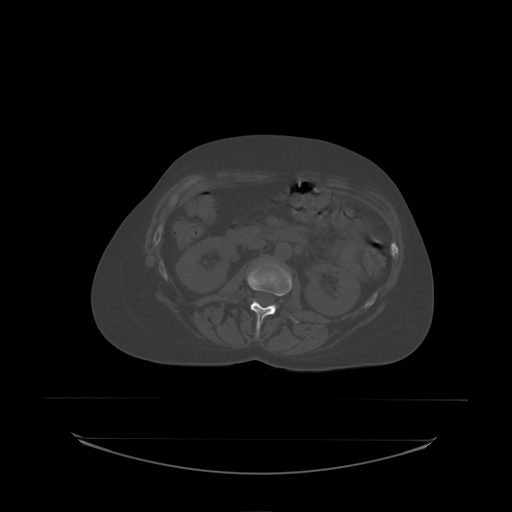
CT including the spine, one axial slice. Slice 70 of 242 in the series (ordered by position). Bone window (W 1800 / L 400 HU). 2.5 mm slice thickness. 512 × 512 image matrix, field of view 500 × 500 mm. Patient: female, 53 years. From the clinical record (not read from this slice): primary cancer: lung.
Outlined on this slice (semi-automatic segmentation, software-assisted and operator-edited):
- L2 vertebra: bounding box [x1, y1, x2, y2] px = [248, 261, 299, 338]